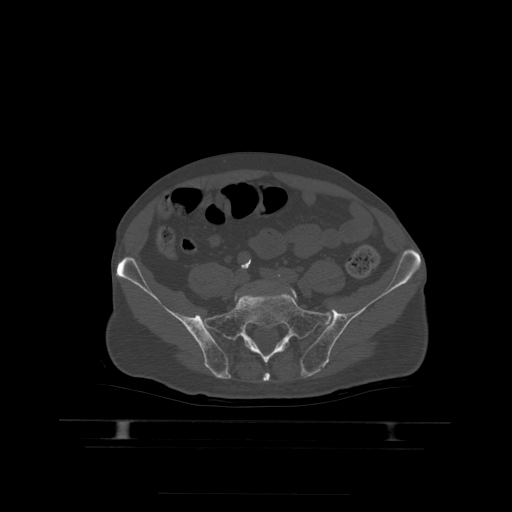
CT including the spine, one axial slice; slice 53 of 522 in the series (ordered by position); bone window (W 1800 / L 400 HU); 1.25 mm slice thickness; 512 × 512 image matrix. Patient age 68 years. Case-level facts recorded for this patient, not image findings: primary cancer: urothelial.
Annotated regions visible in this slice (semi-automatic segmentation, software-assisted and operator-edited):
- L5 vertebra: box from (x=291, y=288) to (x=298, y=299) px